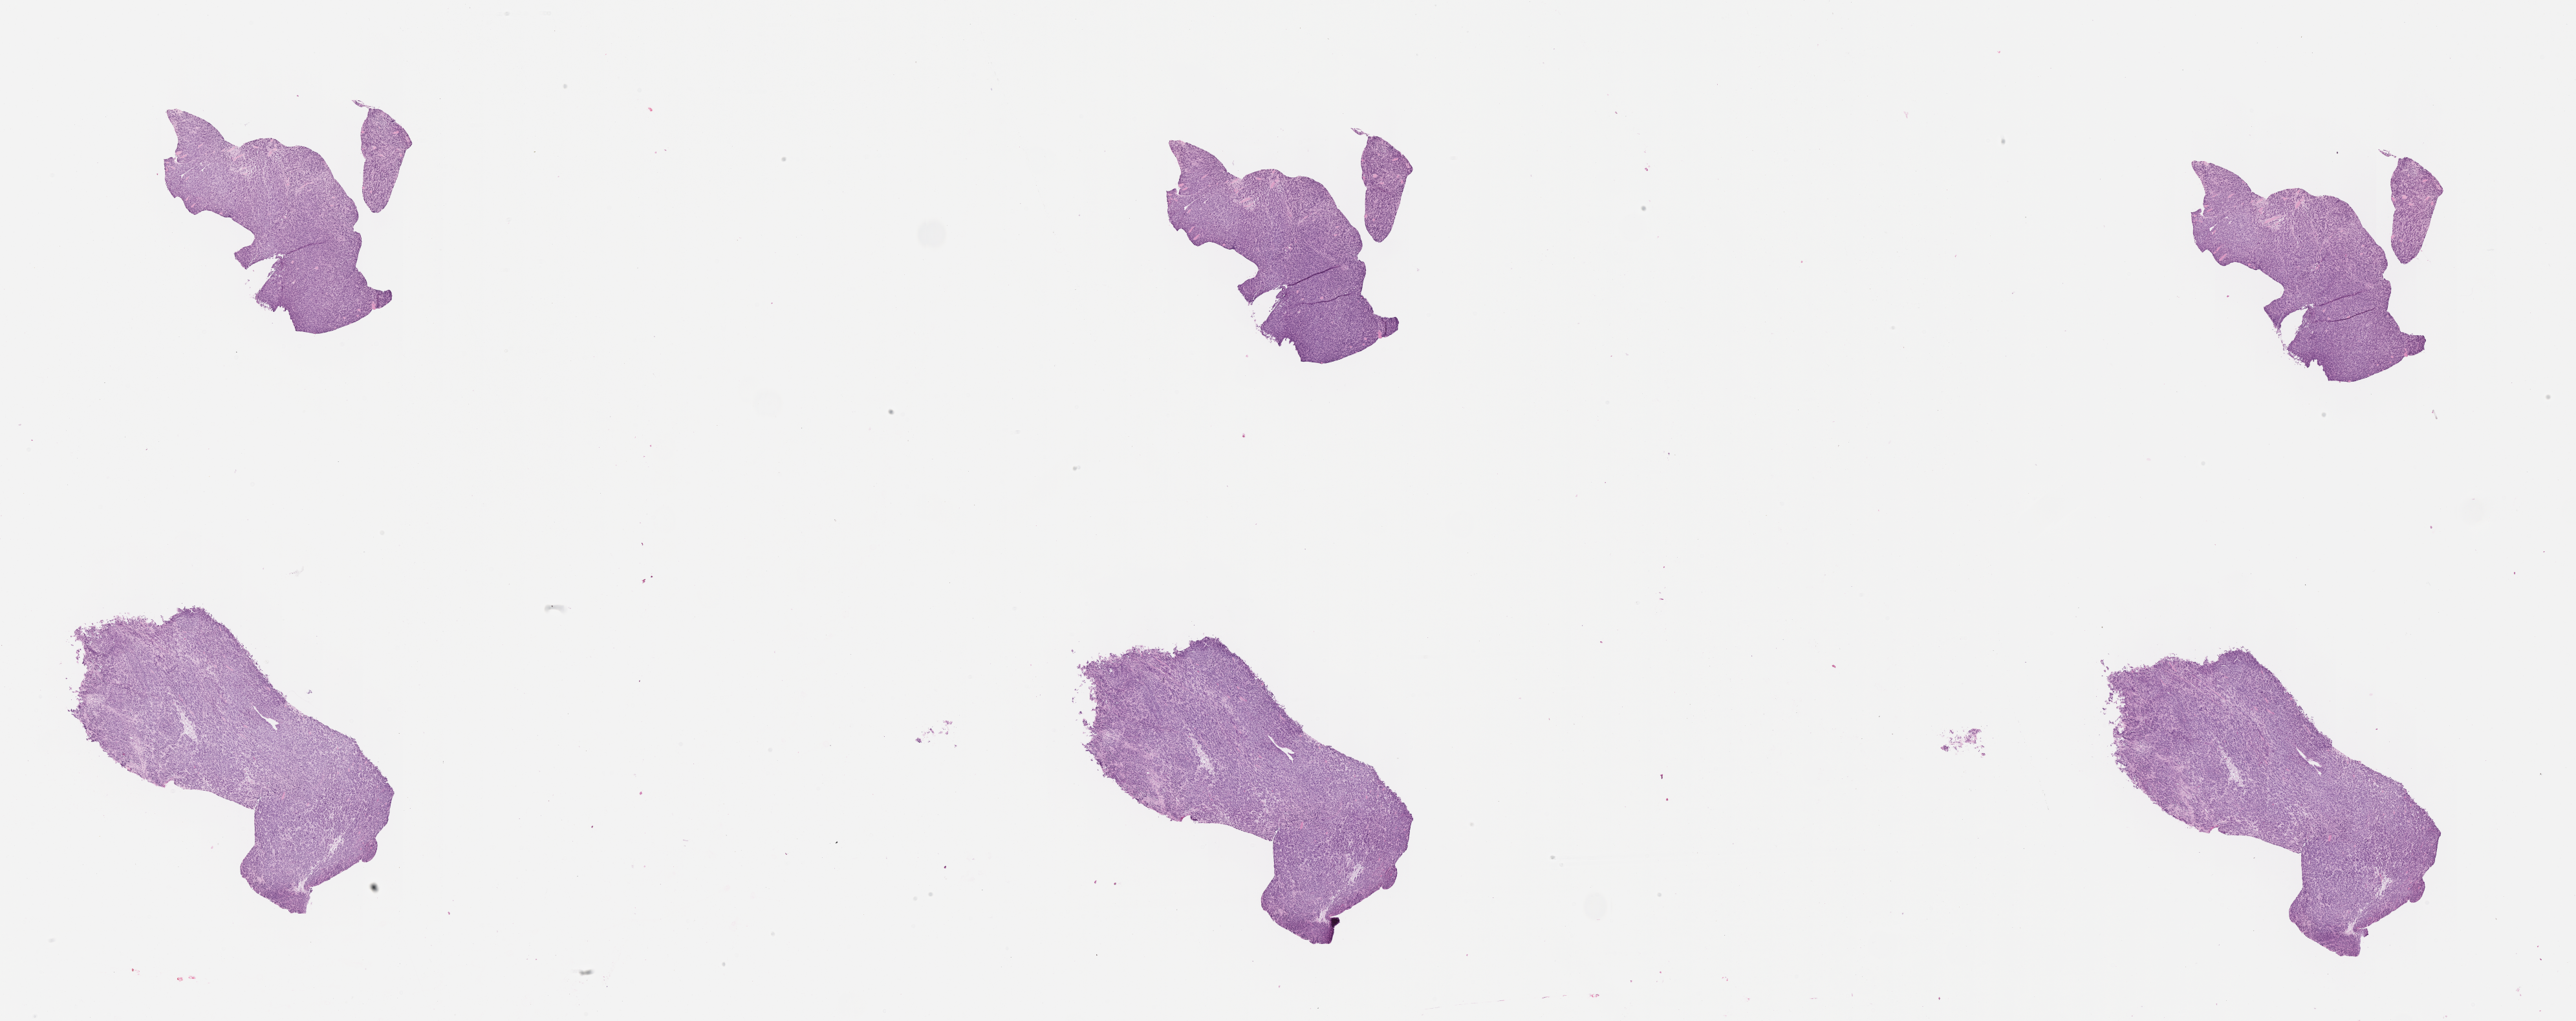
Whole-slide image, haematoxylin and eosin stain of tumor tissue — a low-resolution overview of the entire scanned area, about 32.2 x 12.8 mm; formalin-fixed paraffin-embedded section; sample anatomic site: chest-right. Patient: male, age 2.4 years at diagnosis.
- diagnosis: rhabdomyosarcoma; histological classification: embryonal rhabdomyosarcoma
- metastatic status at presentation (as recorded): non-metastatic
- primary site (case record): chest Wall
- stage (as recorded): 2